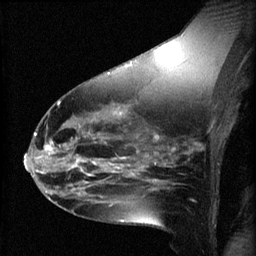
Breast MRI (dynamic contrast-enhanced), one sagittal slice. Slice 32 of 60 in the series (ordered by position). 3 images stored at this slice position (order not interpretable as contrast timing). 1.5 T. TE 4.2 ms, TR 8.2 ms. 256 × 256 image matrix, field of view 180 × 180 mm. Patient: female, 49 years.
Outlined on this slice (semi-automatic segmentation, software-assisted and operator-edited):
- analysis volume of interest (the breast-tissue region the enhancement analysis was run in; not a lesion): bounding box [x1, y1, x2, y2] px = [45, 136, 109, 187]
- tumour enhancement mask (voxels above the 70 % enhancement threshold inside the analysis volume of interest): [45, 142, 109, 187]